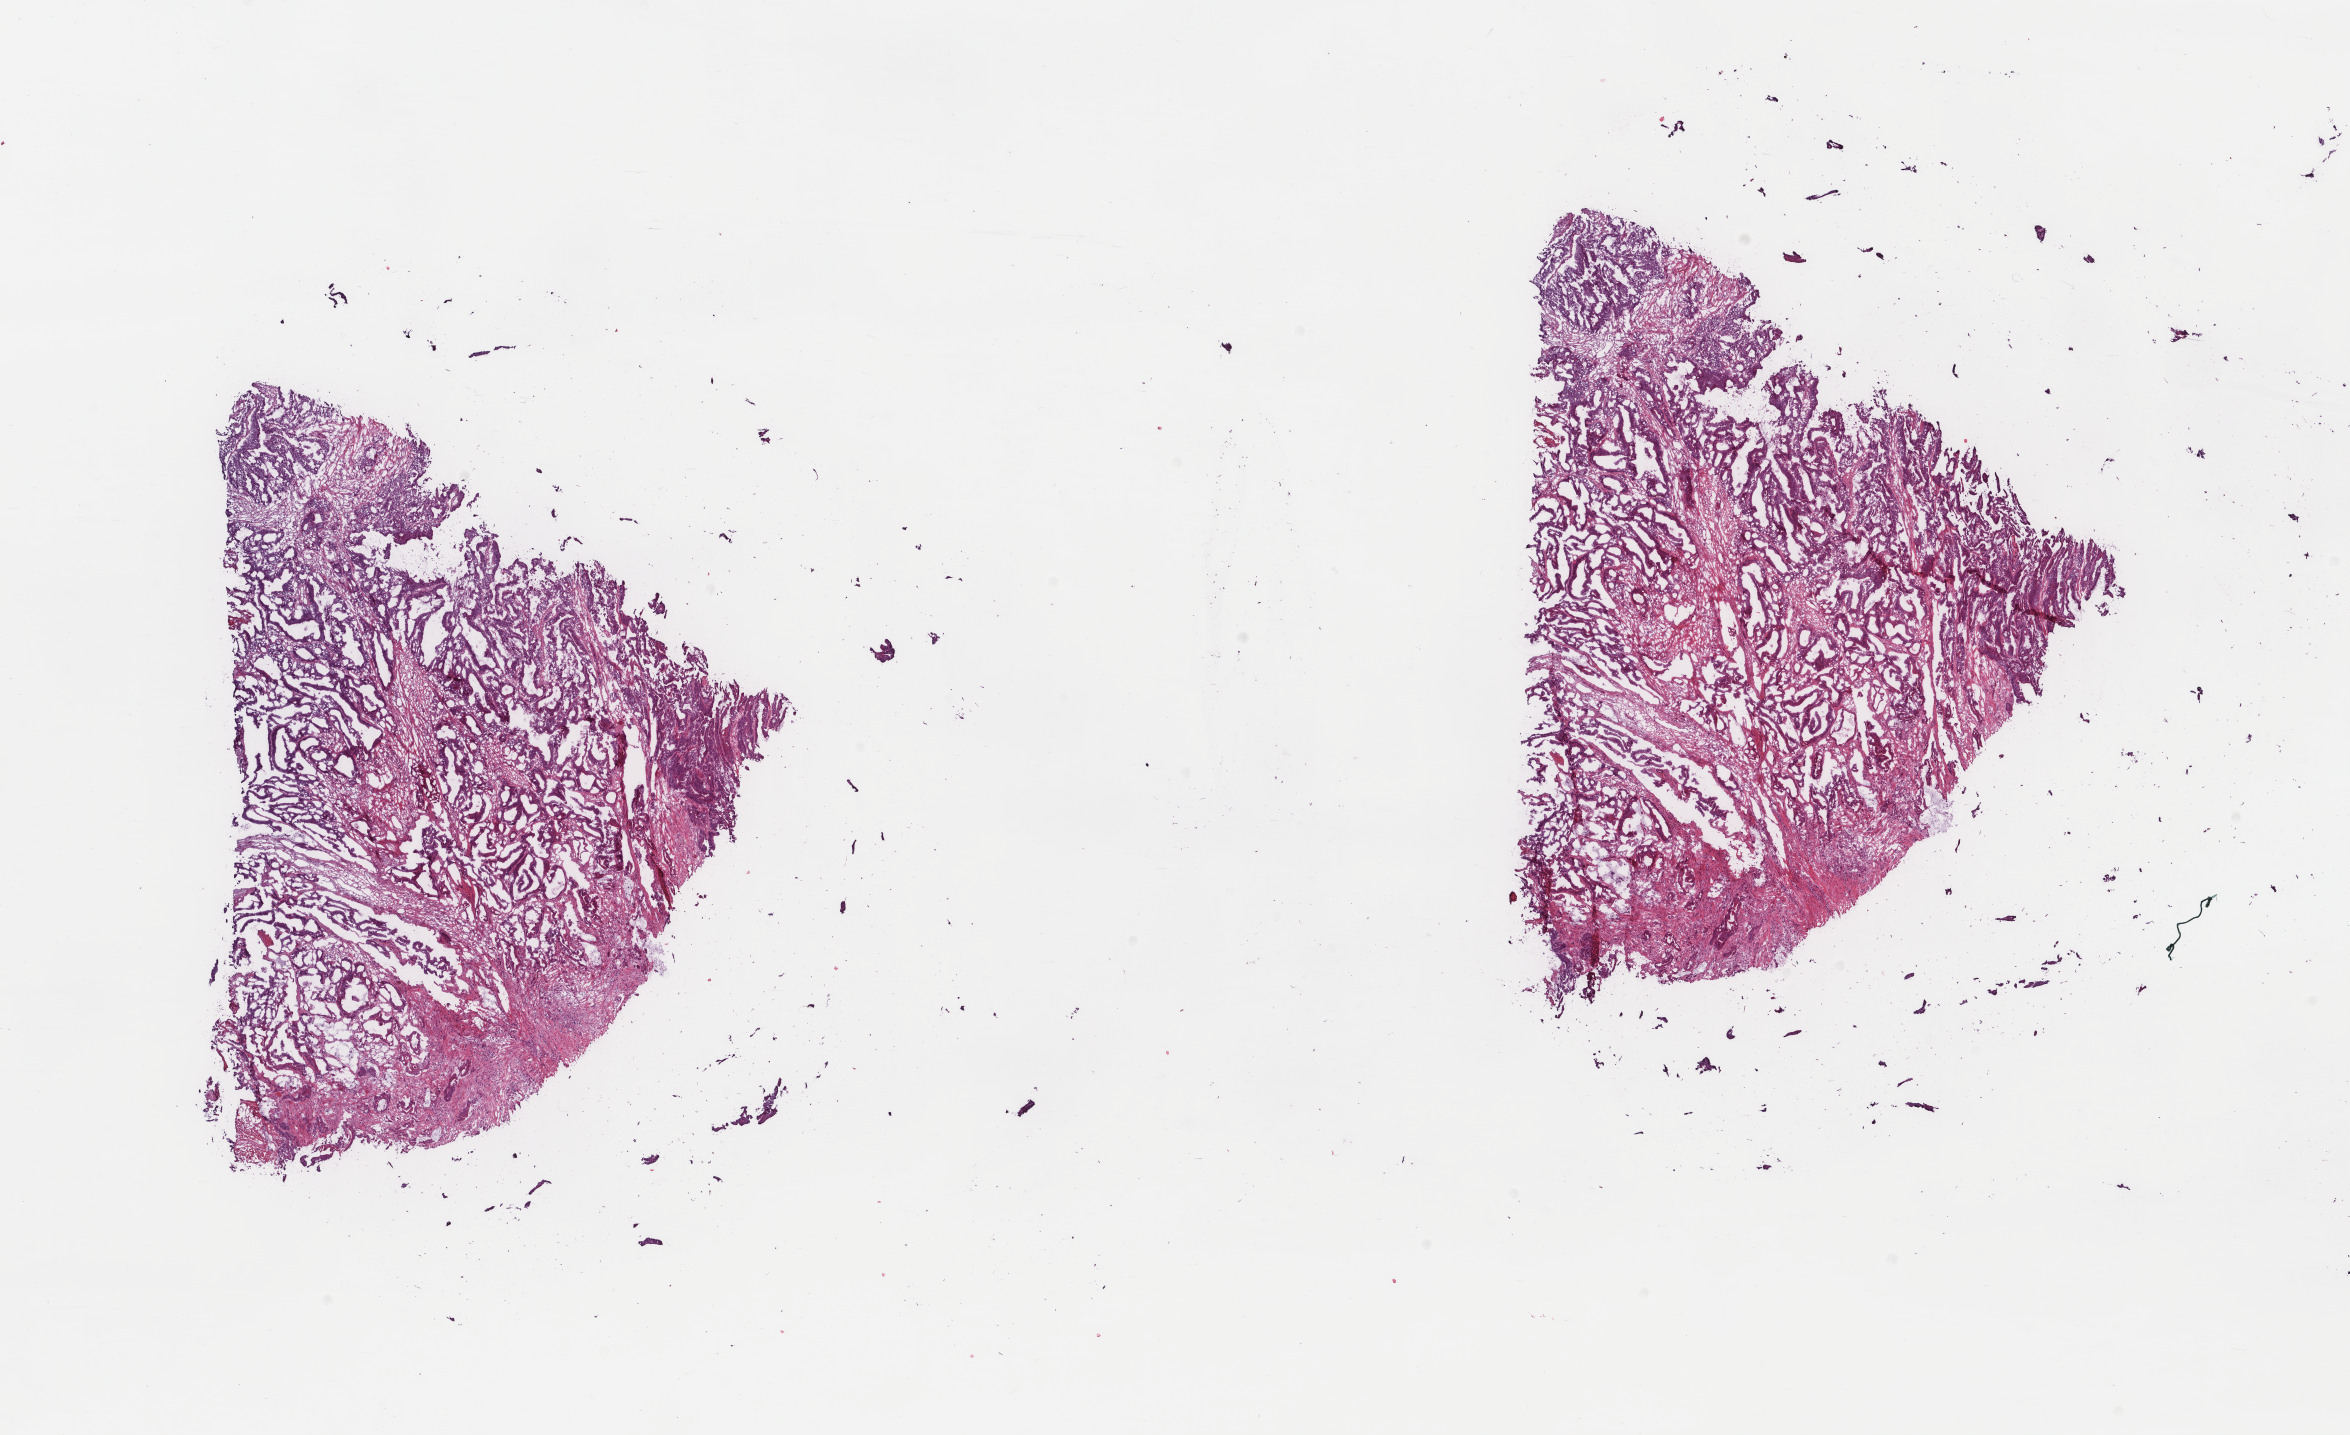
H&E whole-slide image, low-resolution overview of the scanned area, about 18.7 x 11.4 mm (from a 40x scan); frozen section from the top of the tissue portion; colon, primary tumour sample. Male, age 63 years at initial diagnosis. Slide review estimates, as recorded: tumour cells 60%, tumour nuclei 60%, normal cells 0%, stromal cells 35%, necrosis 5%. Inflammatory infiltration, as recorded: lymphocyte infiltration 10%, monocyte infiltration 5%, neutrophil infiltration 0%.
Histologic diagnosis: Adenocarcinoma, NOS (descending colon). TNM: T3 N0 M0. AJCC pathologic stage: IIA (6th edition). Lymph nodes positive (case pathology): 0 of 13 examined.